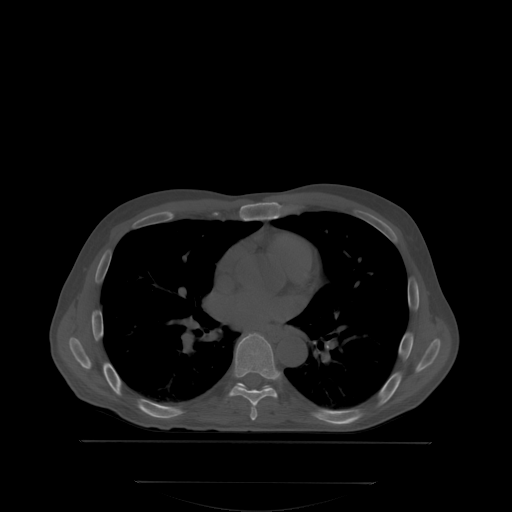
CT including the spine, one axial slice; slice 225 of 350 in the series (ordered by position); bone window (W 1800 / L 400 HU); 2.5 mm slice thickness; 512 × 512 image matrix. Patient: male, 58 years. From the clinical record (not read from this slice): primary cancer: prostate; vertebrae with lytic lesions (as recorded): L1.
Annotated regions visible in this slice (semi-automatically segmented with operator editing):
- T6 vertebra: bounding box (x1, y1, x2, y2) in pixels: (251, 406, 257, 419)
- T7 vertebra: (228, 334, 278, 406)
- T8 vertebra: (237, 384, 269, 388)